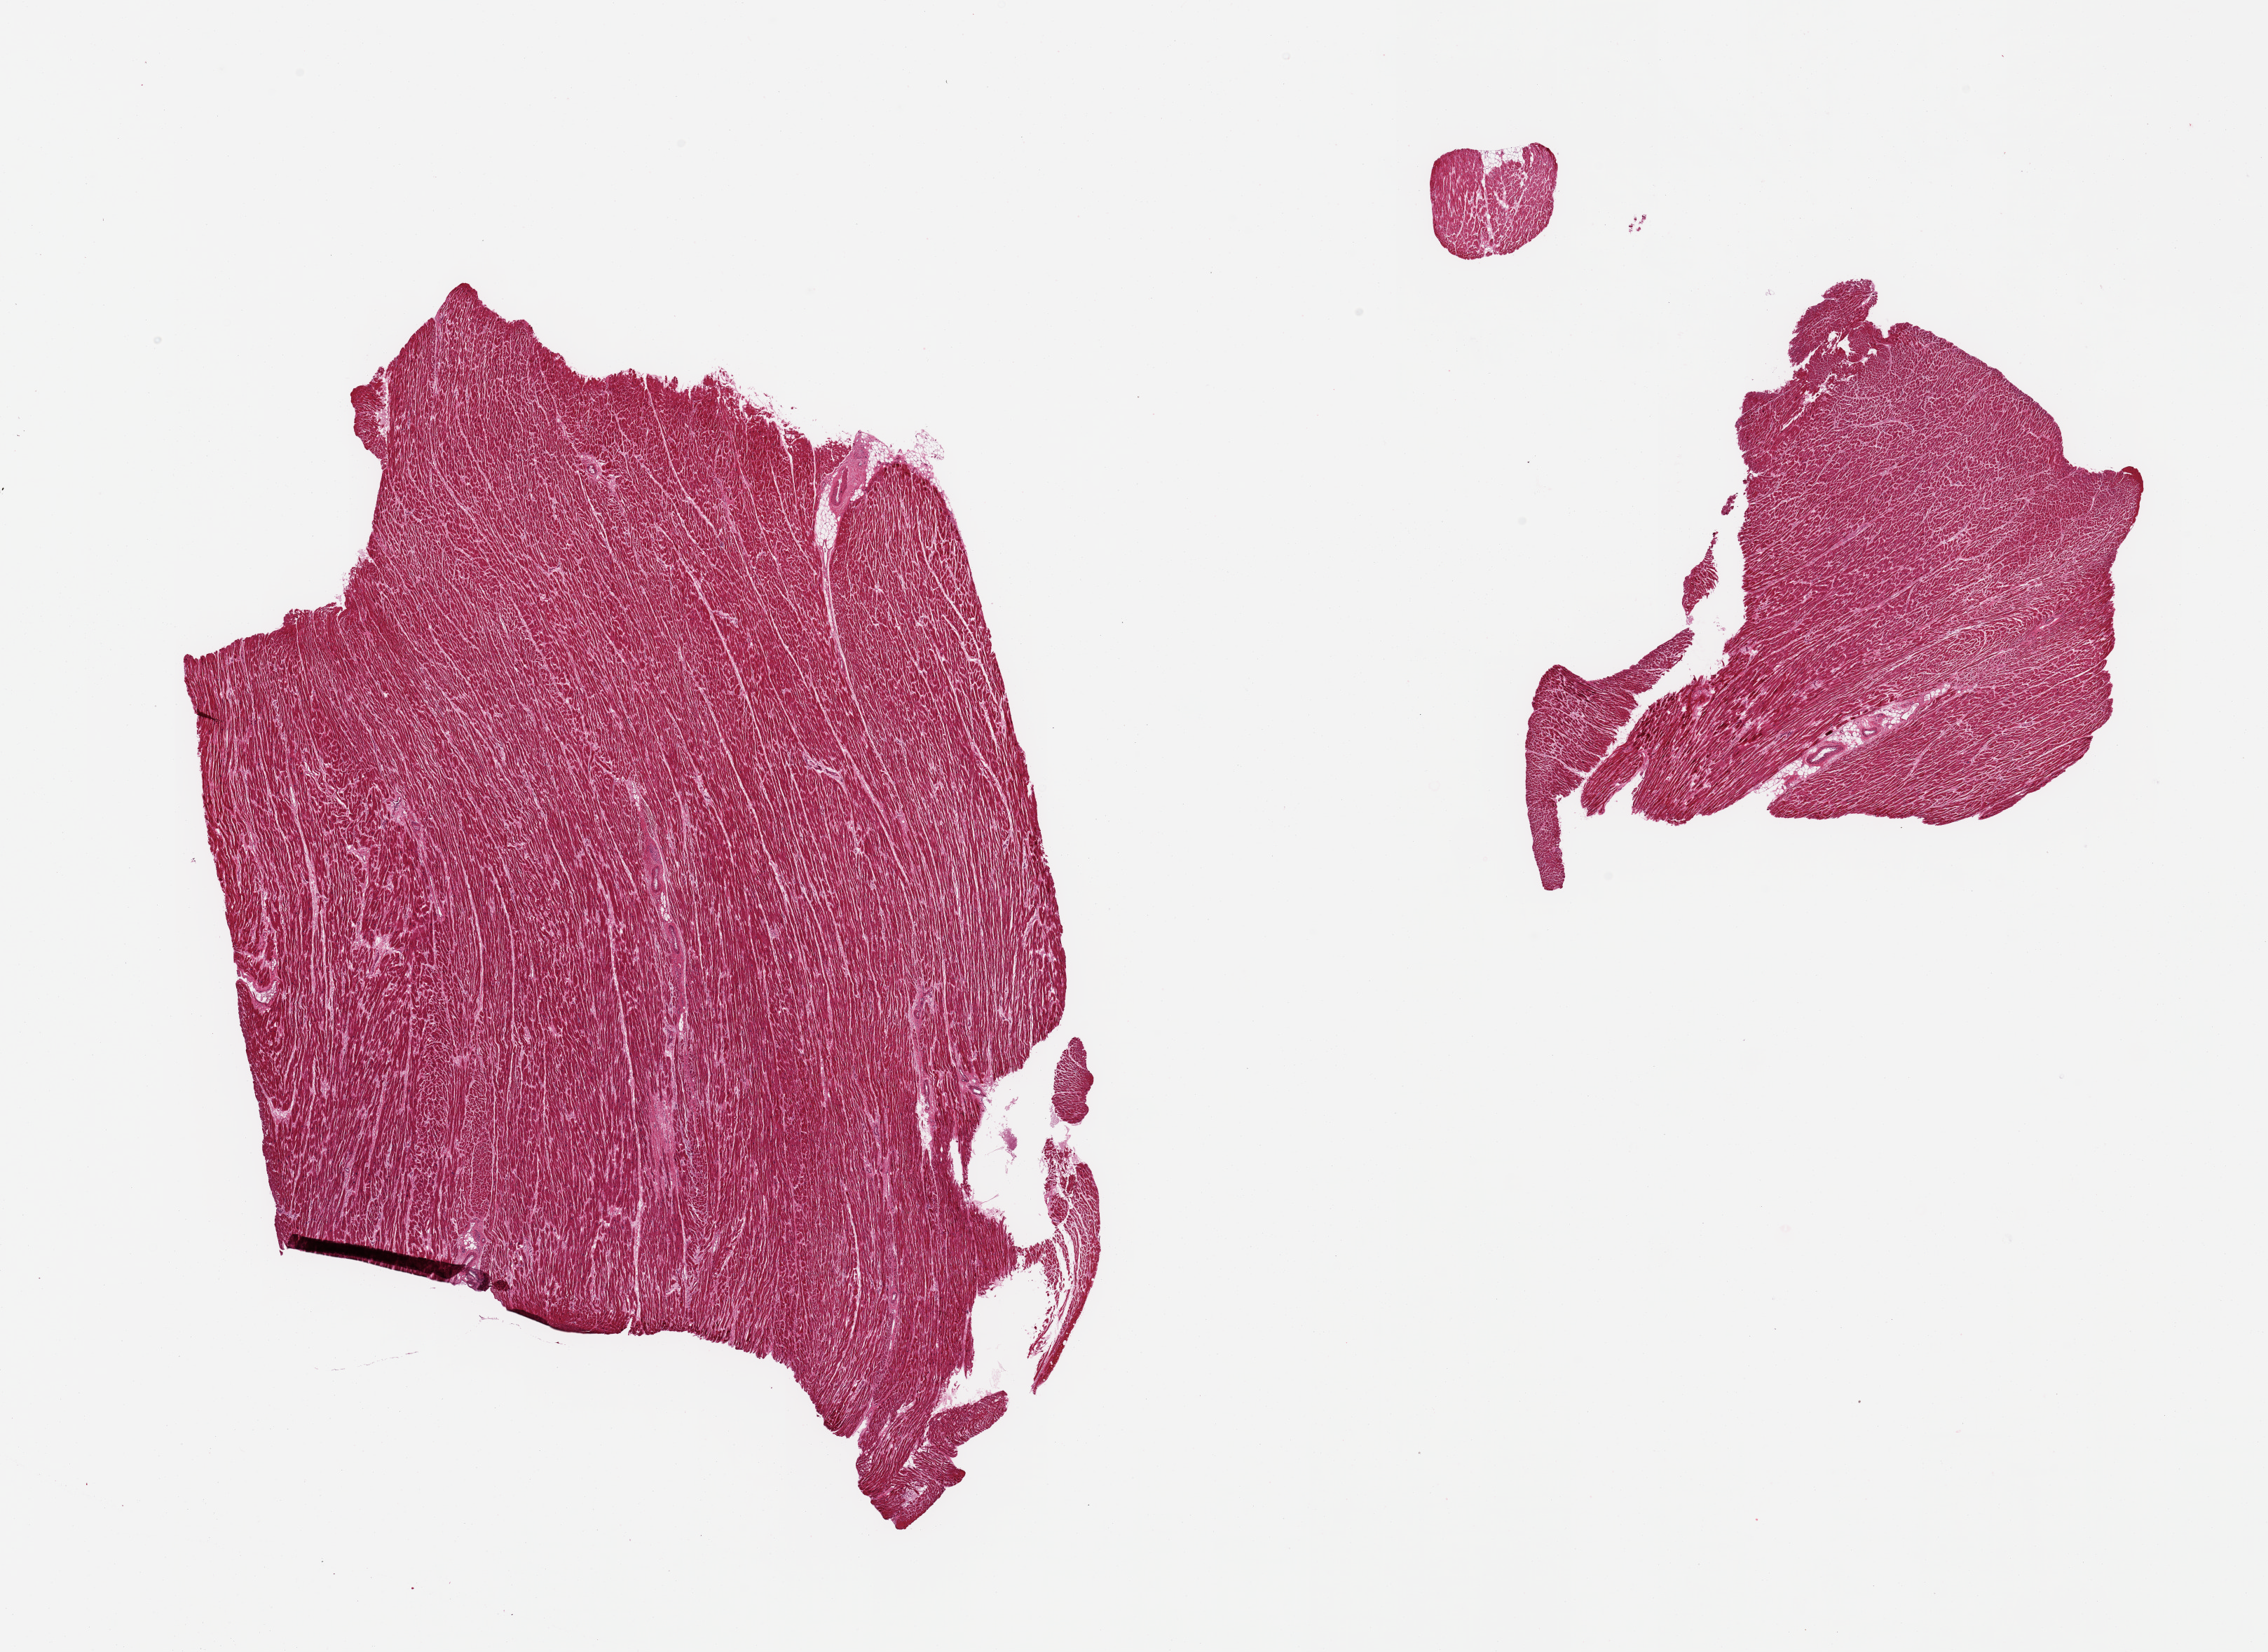
Haematoxylin and eosin whole-slide image, brightfield, whole scanned area (about 25.6 x 18.6 mm, from a 20x scan) shown as a low-resolution overview, PAXgene-fixed, paraffin-embedded tissue, section of heart (target tissue), tissue donor sample. Donor: male.
Review note (as recorded): 2 pieces, moderate interstitial fibrosis/chronic ischemic change.